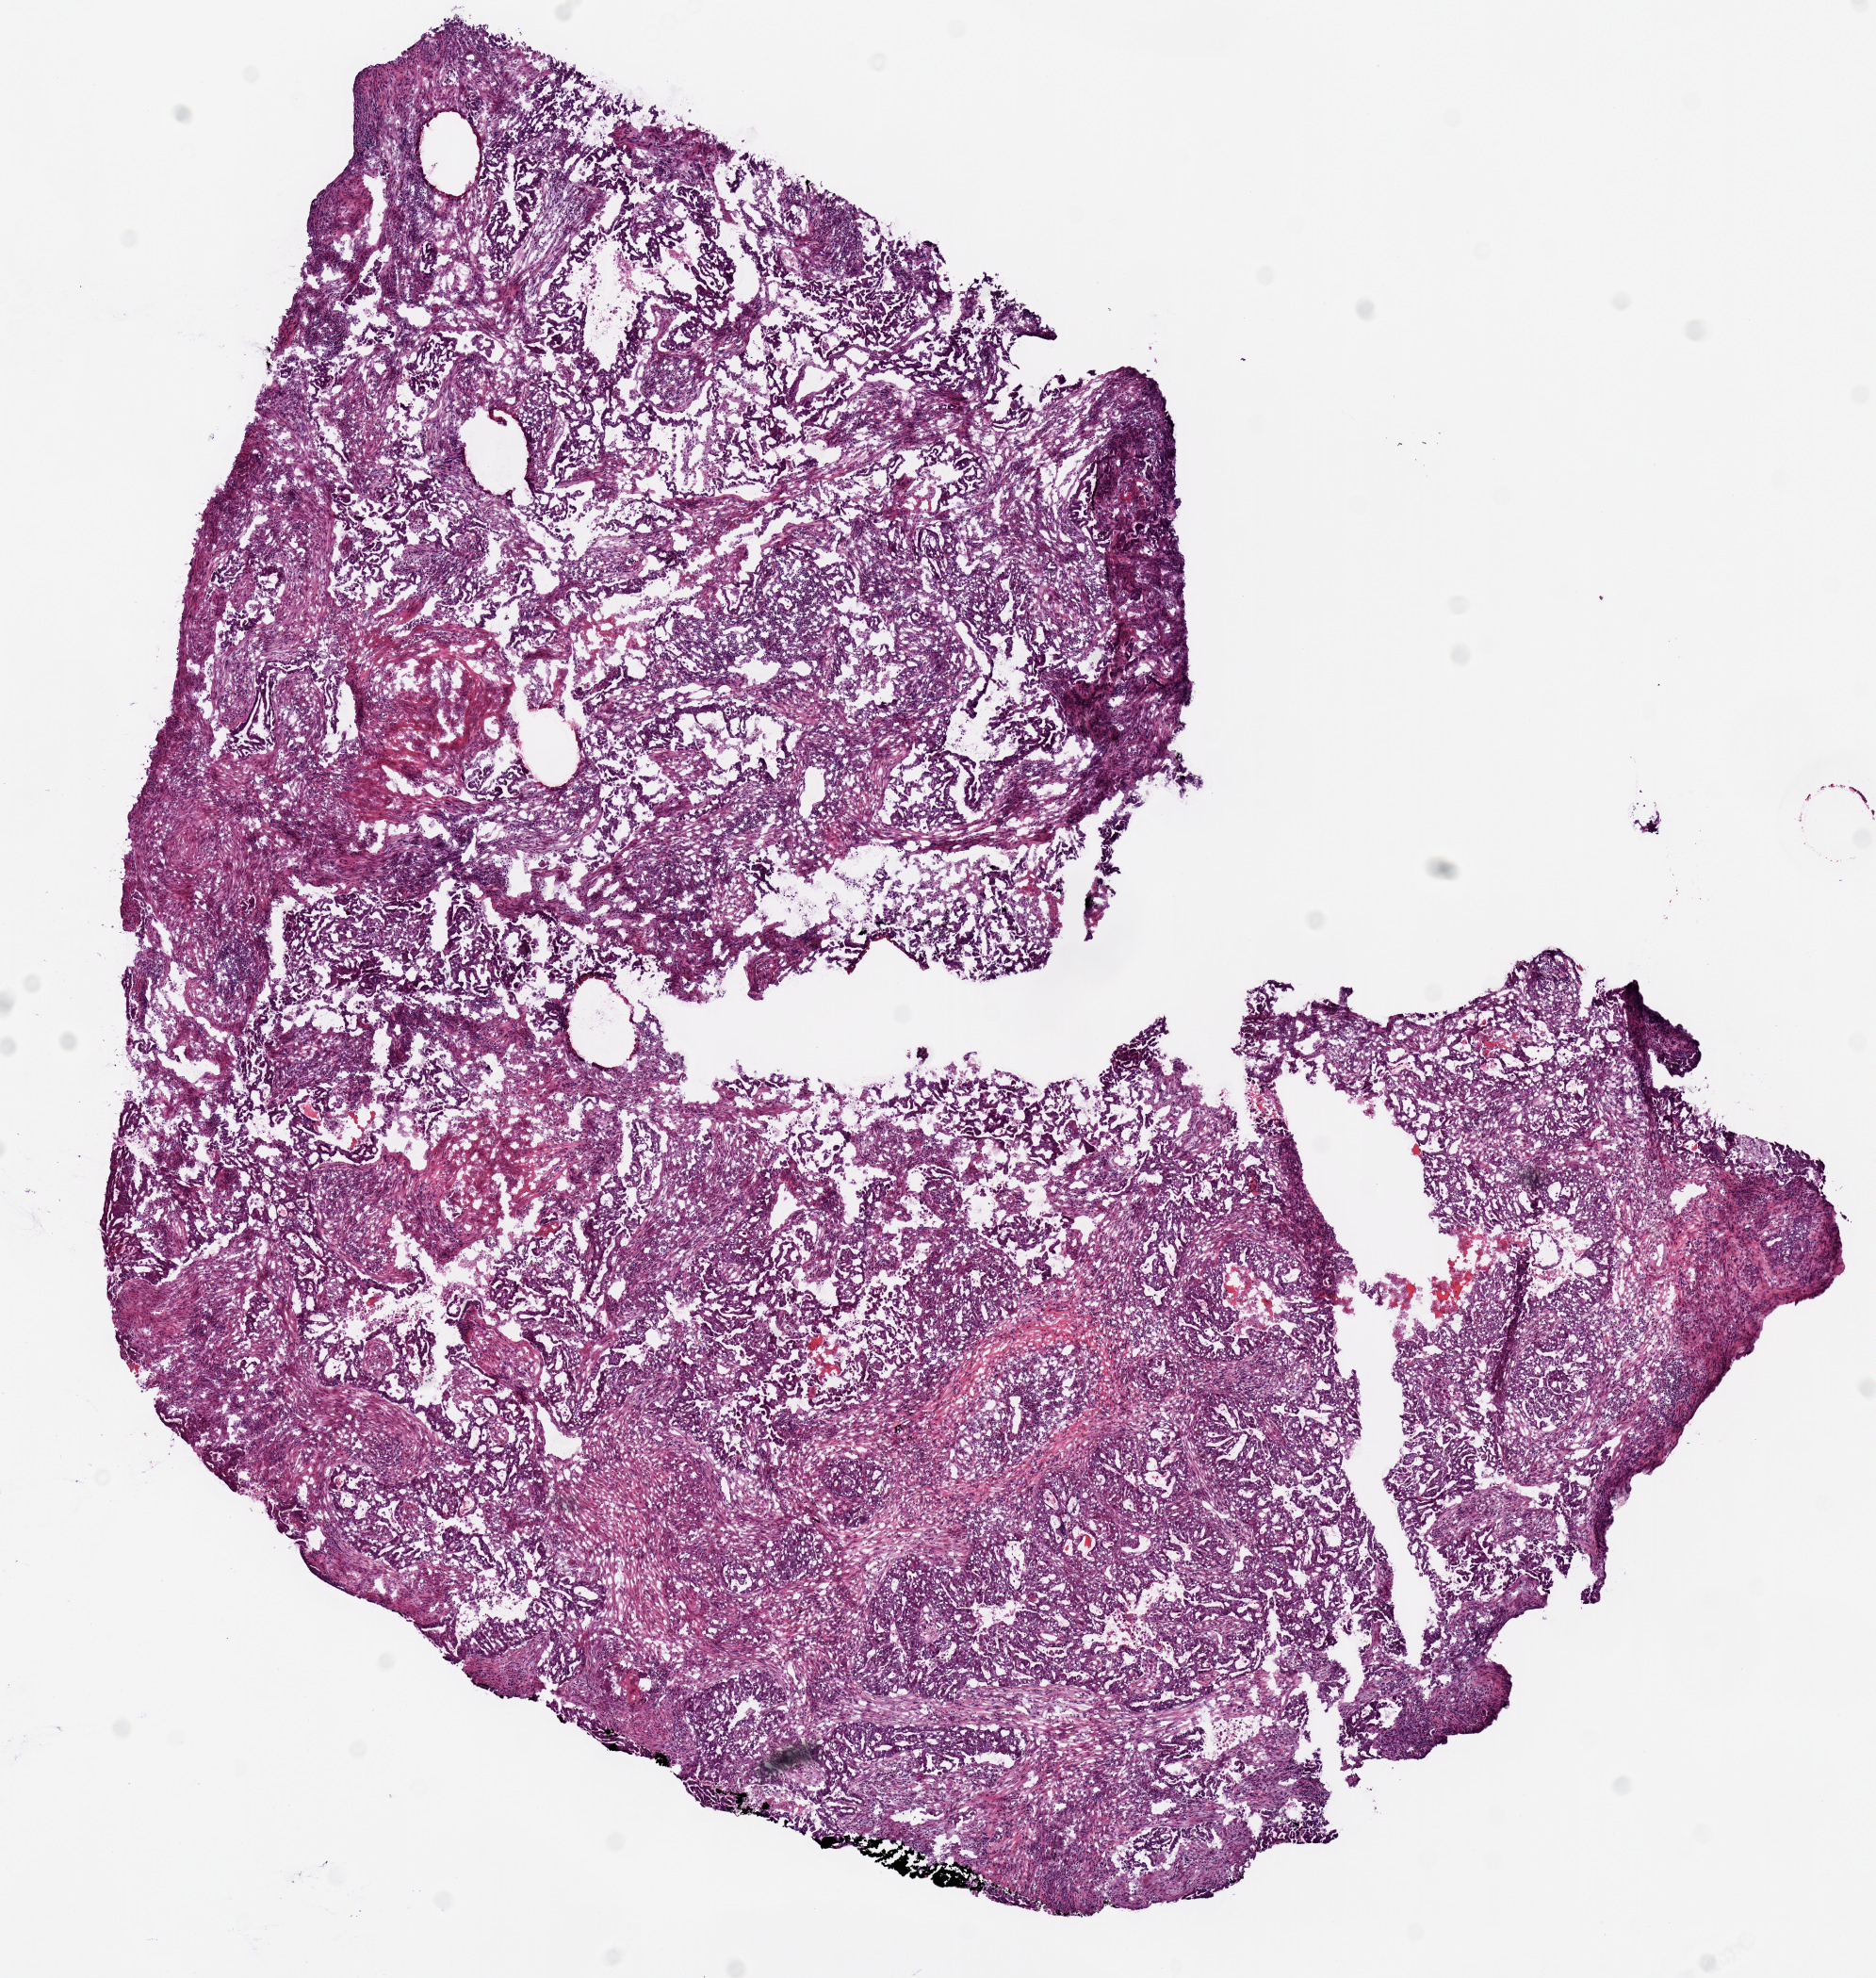
Digitized H&E-stained tissue section (whole slide), whole scanned area (about 7.9 x 8.3 mm, acquisition: 20x scan) shown as a low-resolution overview, frozen section, sample: primary tumour, lung. Male patient; age at initial diagnosis 76 years. Pathologist review of this section (percent, as recorded): tumour nuclei 80%, necrosis 2%. Inflammatory infiltration, as recorded: lymphocyte infiltration 15%.
Laterality: right. AJCC pathologic stage: IB (7th edition). TNM: T2a N0 MX. Histologic diagnosis: Adenocarcinoma, NOS (lower lobe, lung).